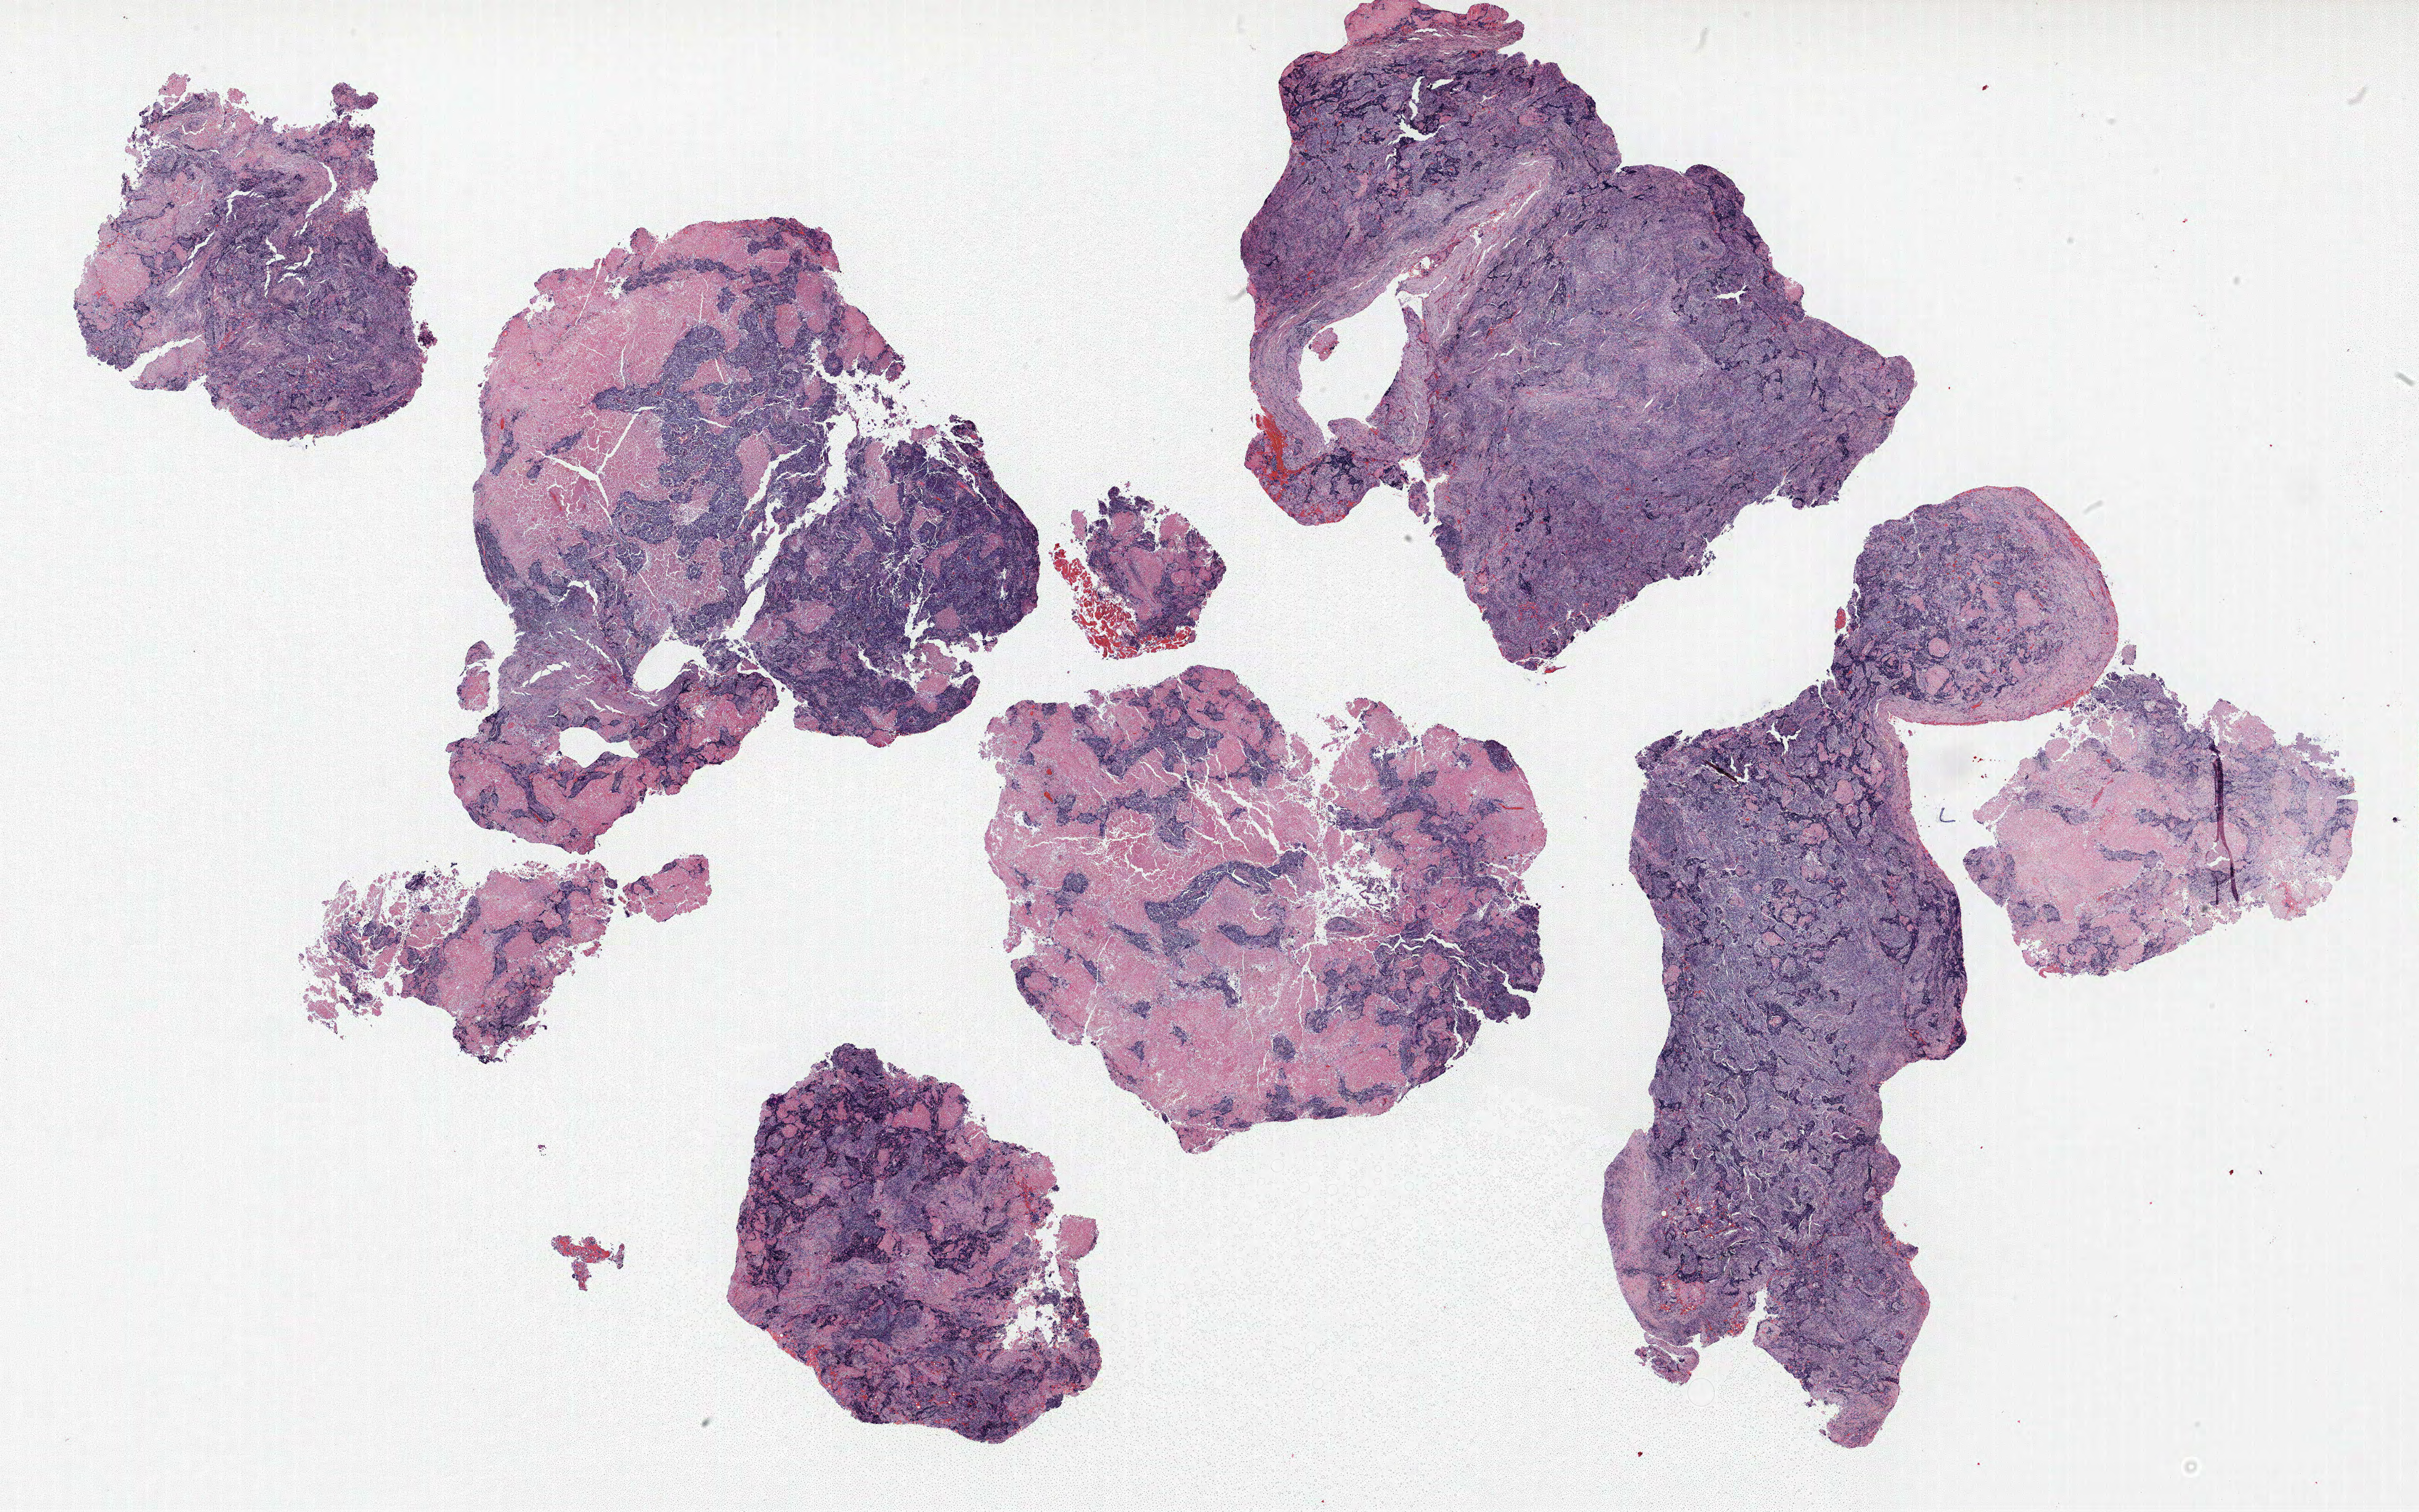
Whole-slide histology image, H&E — low-resolution overview of the scanned area, about 31.4 x 19.7 mm (acquisition: 40x scan), FFPE section, lung tissue. Male patient, aged 59 at enrolment.
Participant's lung-cancer diagnosis: Large cell carcinoma, NOS.